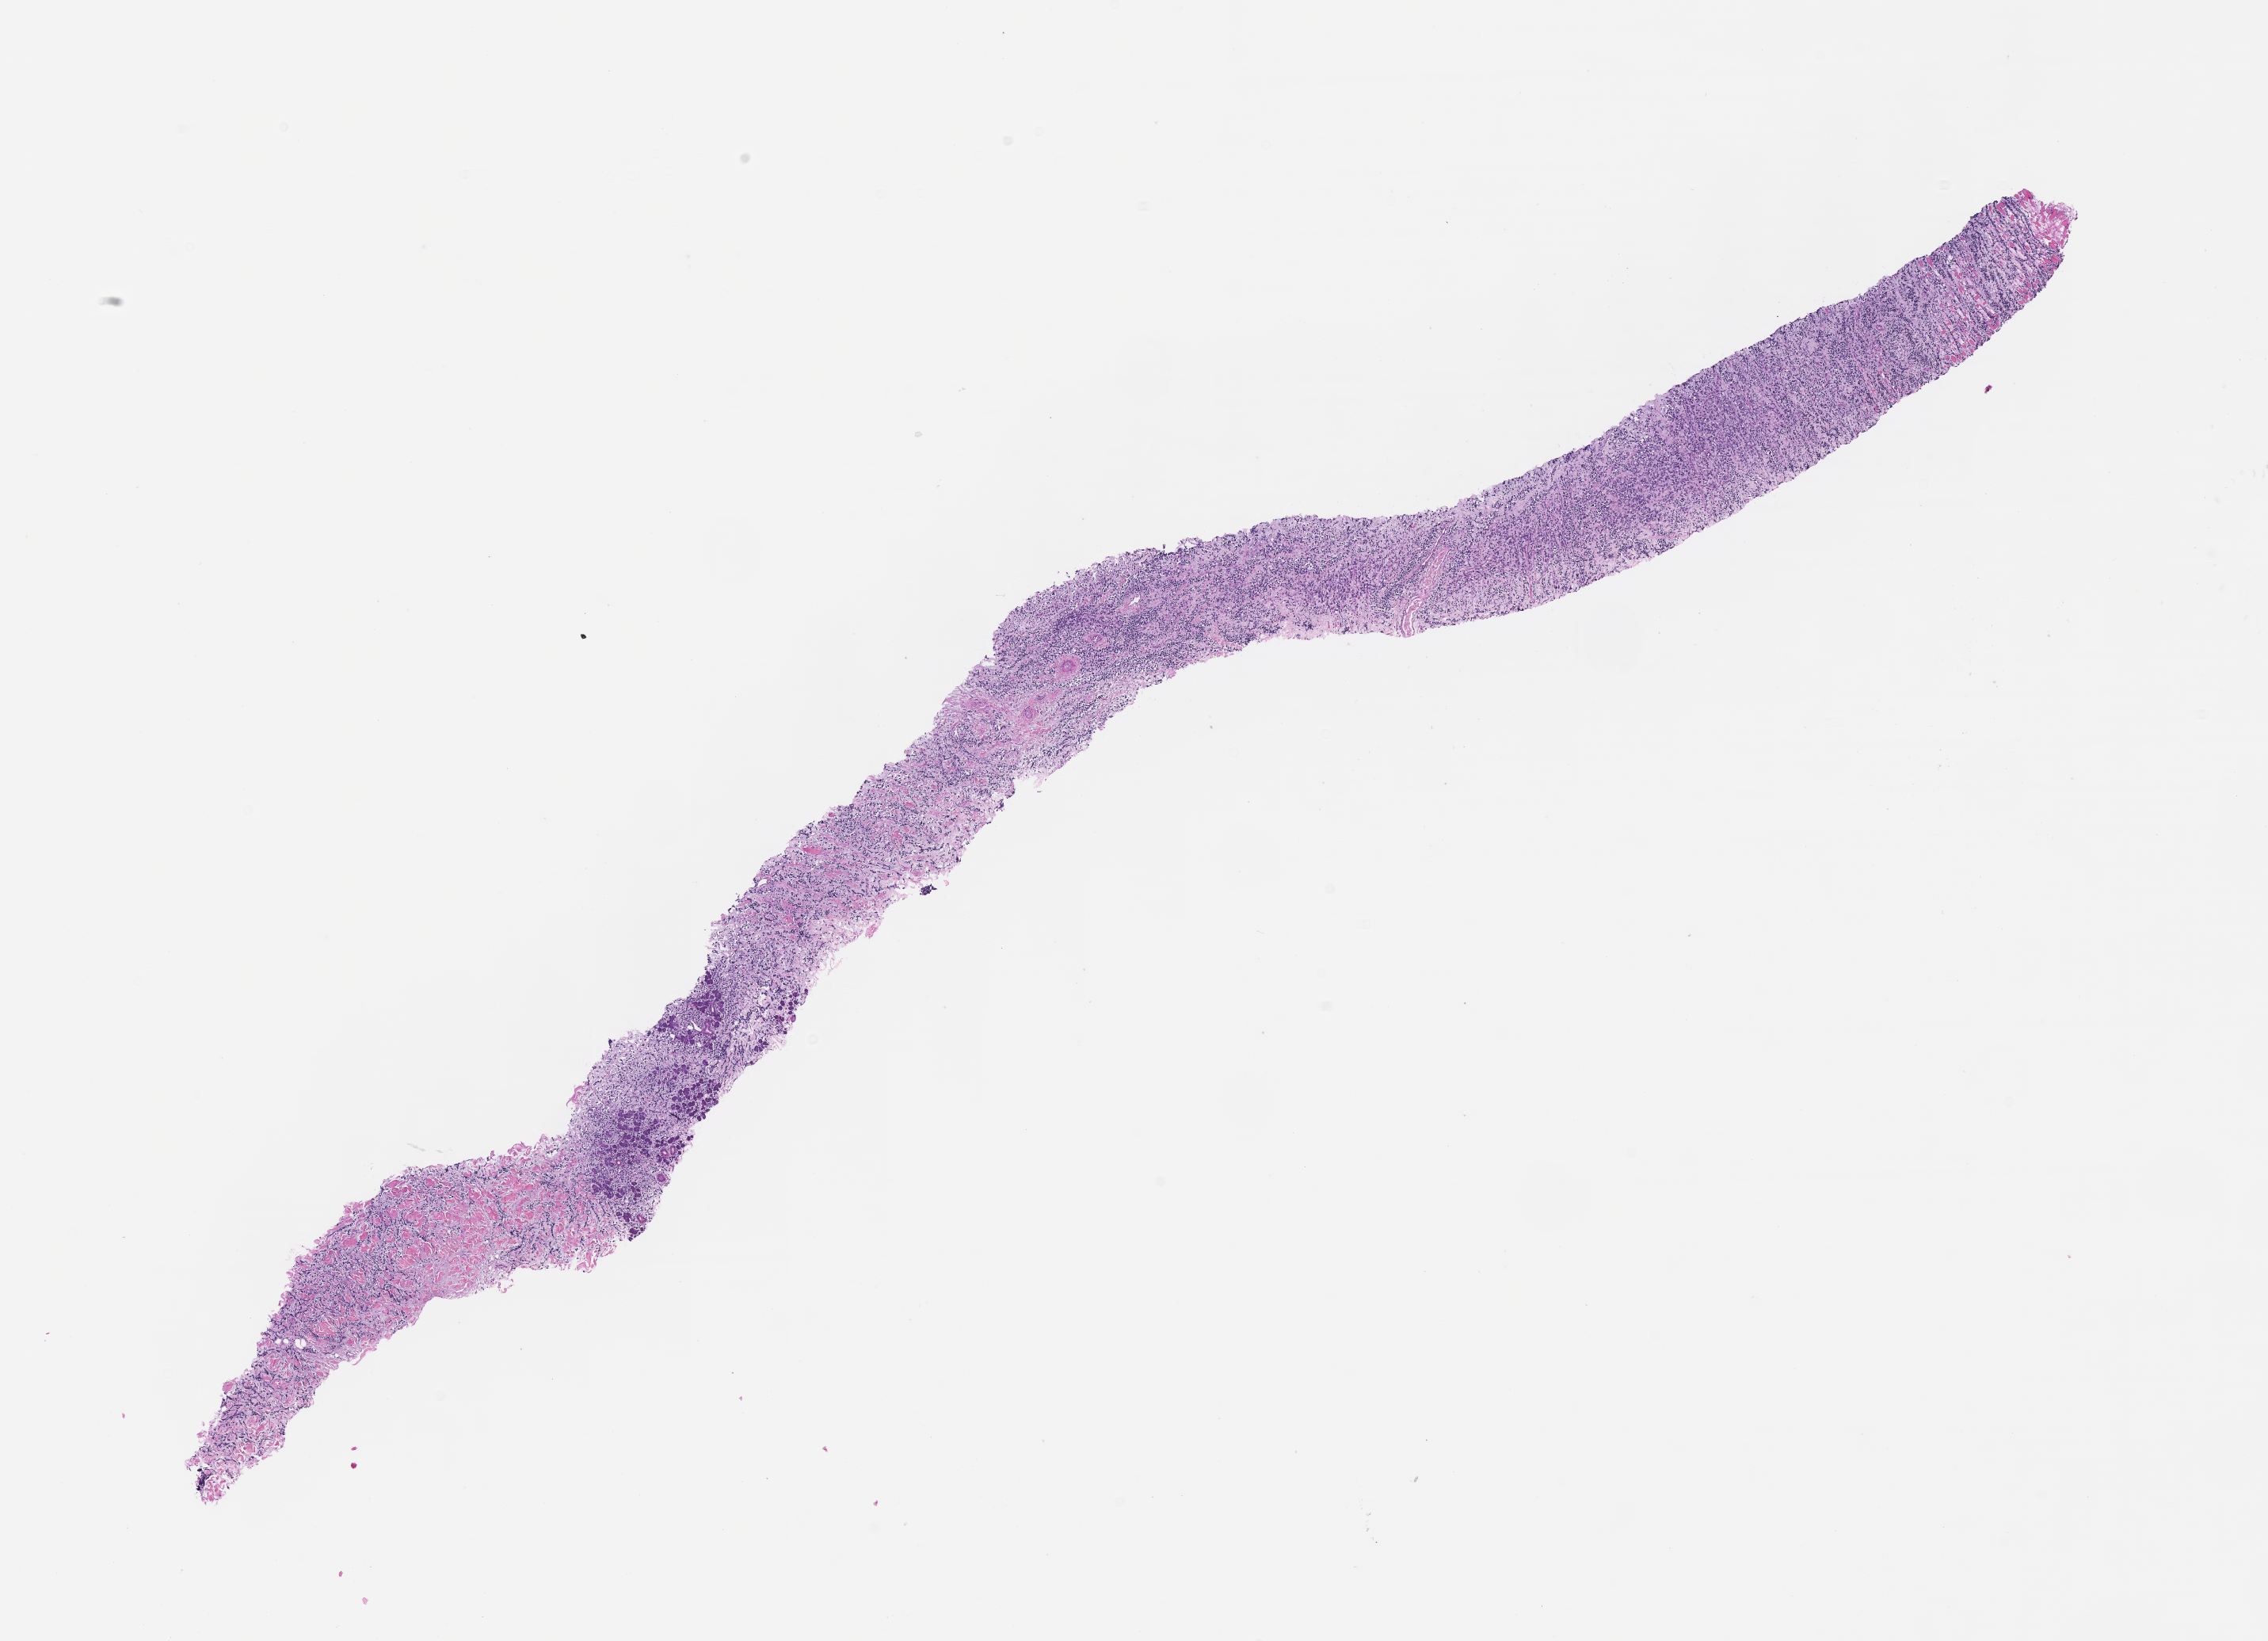
Haematoxylin and eosin whole-slide image of tumor tissue, low-resolution overview of the scanned area, about 11.6 x 8.4 mm. Formalin-fixed paraffin-embedded section. Sample anatomic site: parotid gland-left. Female patient, age at diagnosis 9.2 years.
Stage (as recorded): 3. Primary site (case record): parotid & PM Extension. Metastatic status at presentation (as recorded): non-metastatic. Diagnosis: rhabdomyosarcoma; histological classification: embryonal rhabdomyosarcoma.